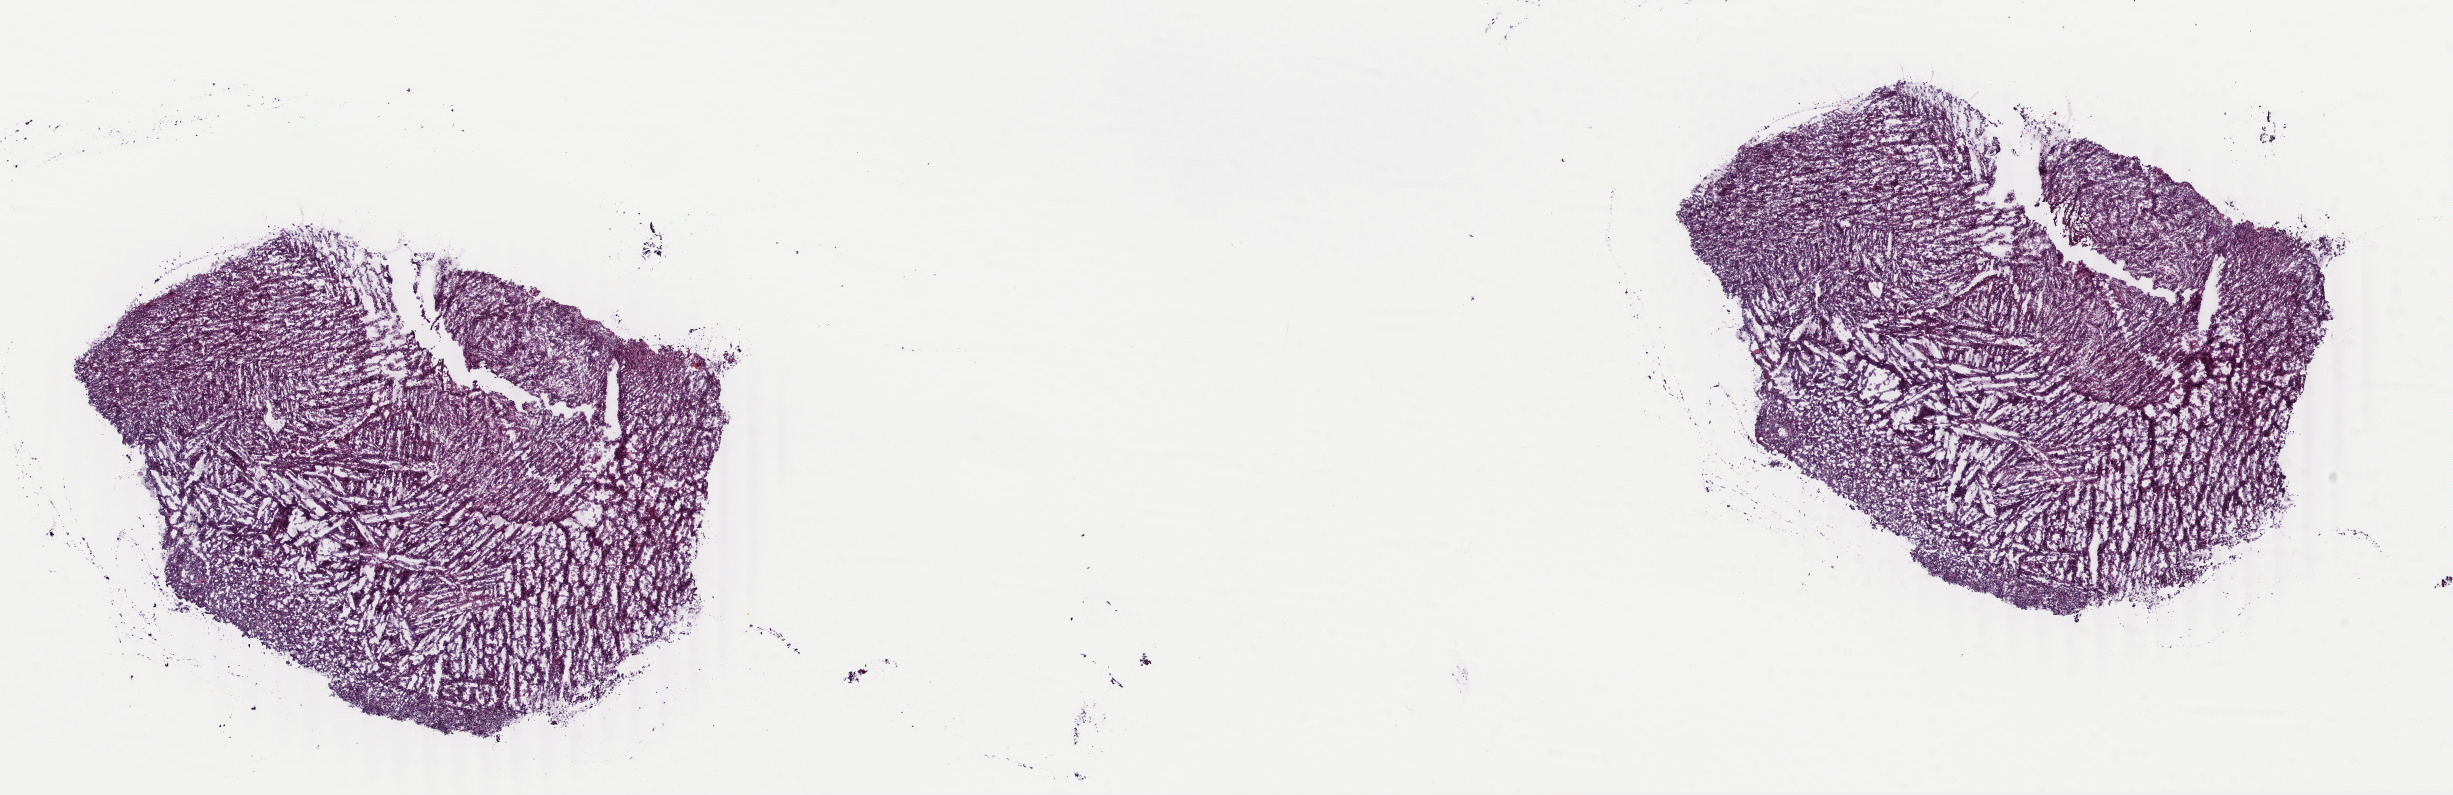
H&E whole-slide image — whole scanned area (about 19.5 x 6.3 mm, from a 40x scan) shown as a low-resolution overview, frozen section, uterus, primary tumour sample. Female, age 69 years at initial diagnosis. Slide review estimates, as recorded: tumour cells 90%, tumour nuclei 95%, normal cells 0%, stromal cells 5%, necrosis 5%. Inflammatory infiltration, as recorded: lymphocyte infiltration 0%, monocyte infiltration 0%, neutrophil infiltration 0%.
Pathologic diagnosis: Mullerian mixed tumor. FIGO stage: IA.